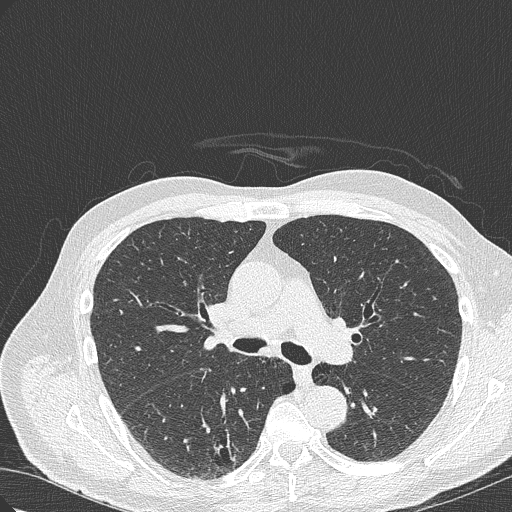
Low-dose screening chest CT, axial slice, baseline annual screen, lung window (W 1500 / L -600 HU), lung (sharp) reconstruction kernel (B50f), 120 kVp, slice 122 of 322 in the series, 512 × 512 image matrix, field of view 350 × 350 mm. Male participant, aged 70 years at enrolment.
Lesion marked by an expert reader, bounding box (x1, y1, x2, y2) in pixels: (200, 419, 264, 470). The screening reader recorded 4 non-calcified nodules or masses ≥4 mm on this exam; which of them this box marks is not recorded. Later outcome: lung cancer diagnosed 978 days after this screen (after the third annual screen) — bronchiolo-alveolar adenocarcinoma, NOS, right lower lobe, poorly differentiated (G3), stage IB (AJCC 6th edition), 30 mm at pathology.